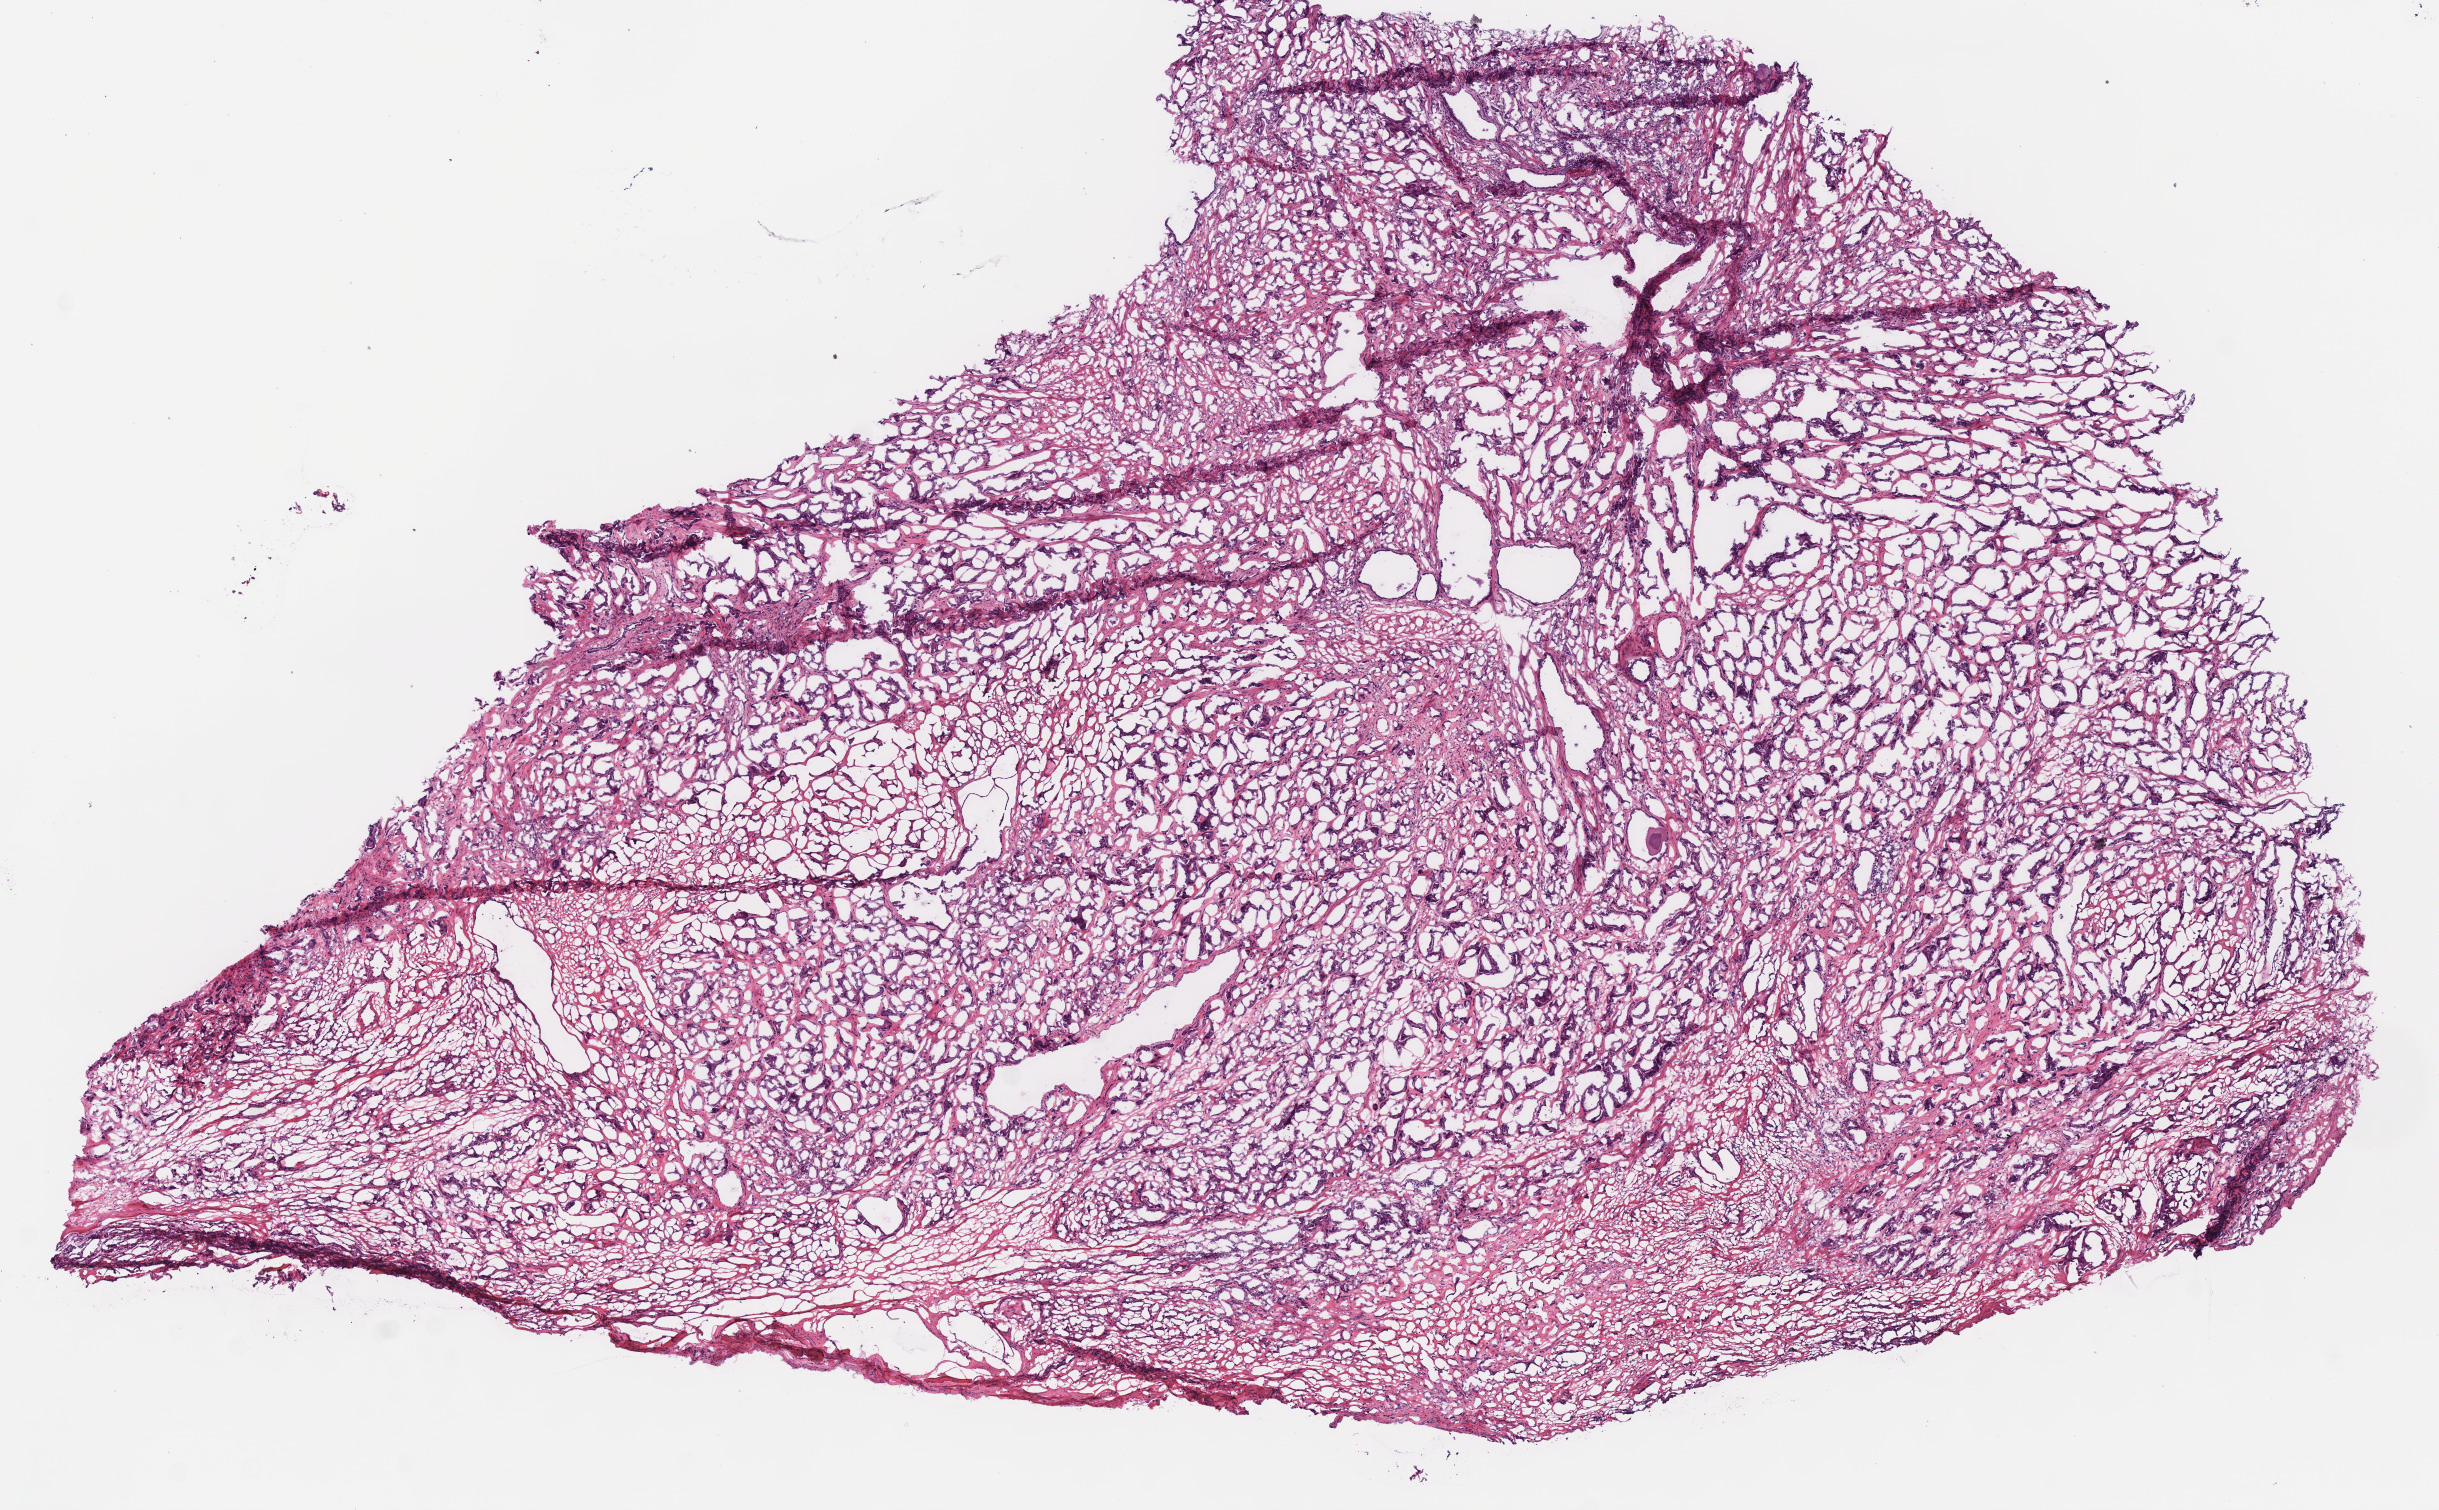
Whole-slide histology image, Hematoxylin and eosin (H&E) stained — whole scanned area (about 9.6 x 5.9 mm, from a 40x scan) shown as a low-resolution overview; frozen section; sample: primary tumour, prostate. Male patient; age at initial diagnosis 52 years.
Histologic diagnosis: Acinar cell carcinoma.